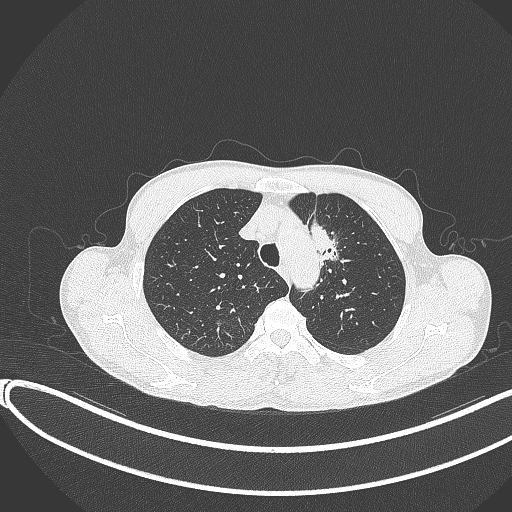
Chest CT, one axial slice. Position 302 of 374 along the scan axis. Reconstruction kernel B70f. 120 kVp. Lung window (W 1500 / L -600 HU). 1 mm slice thickness. 512 × 512 image matrix. Patient: male, 58 years. From the clinical record (not read from this slice): clinical TNM (as recorded): T1c N1 M0.
Structures marked on this image (bounding box drawn by a radiologist):
- lung tumour (recorded histology: adenocarcinoma): bounding box <301,220,344,271> (left, top, right, bottom; pixels)